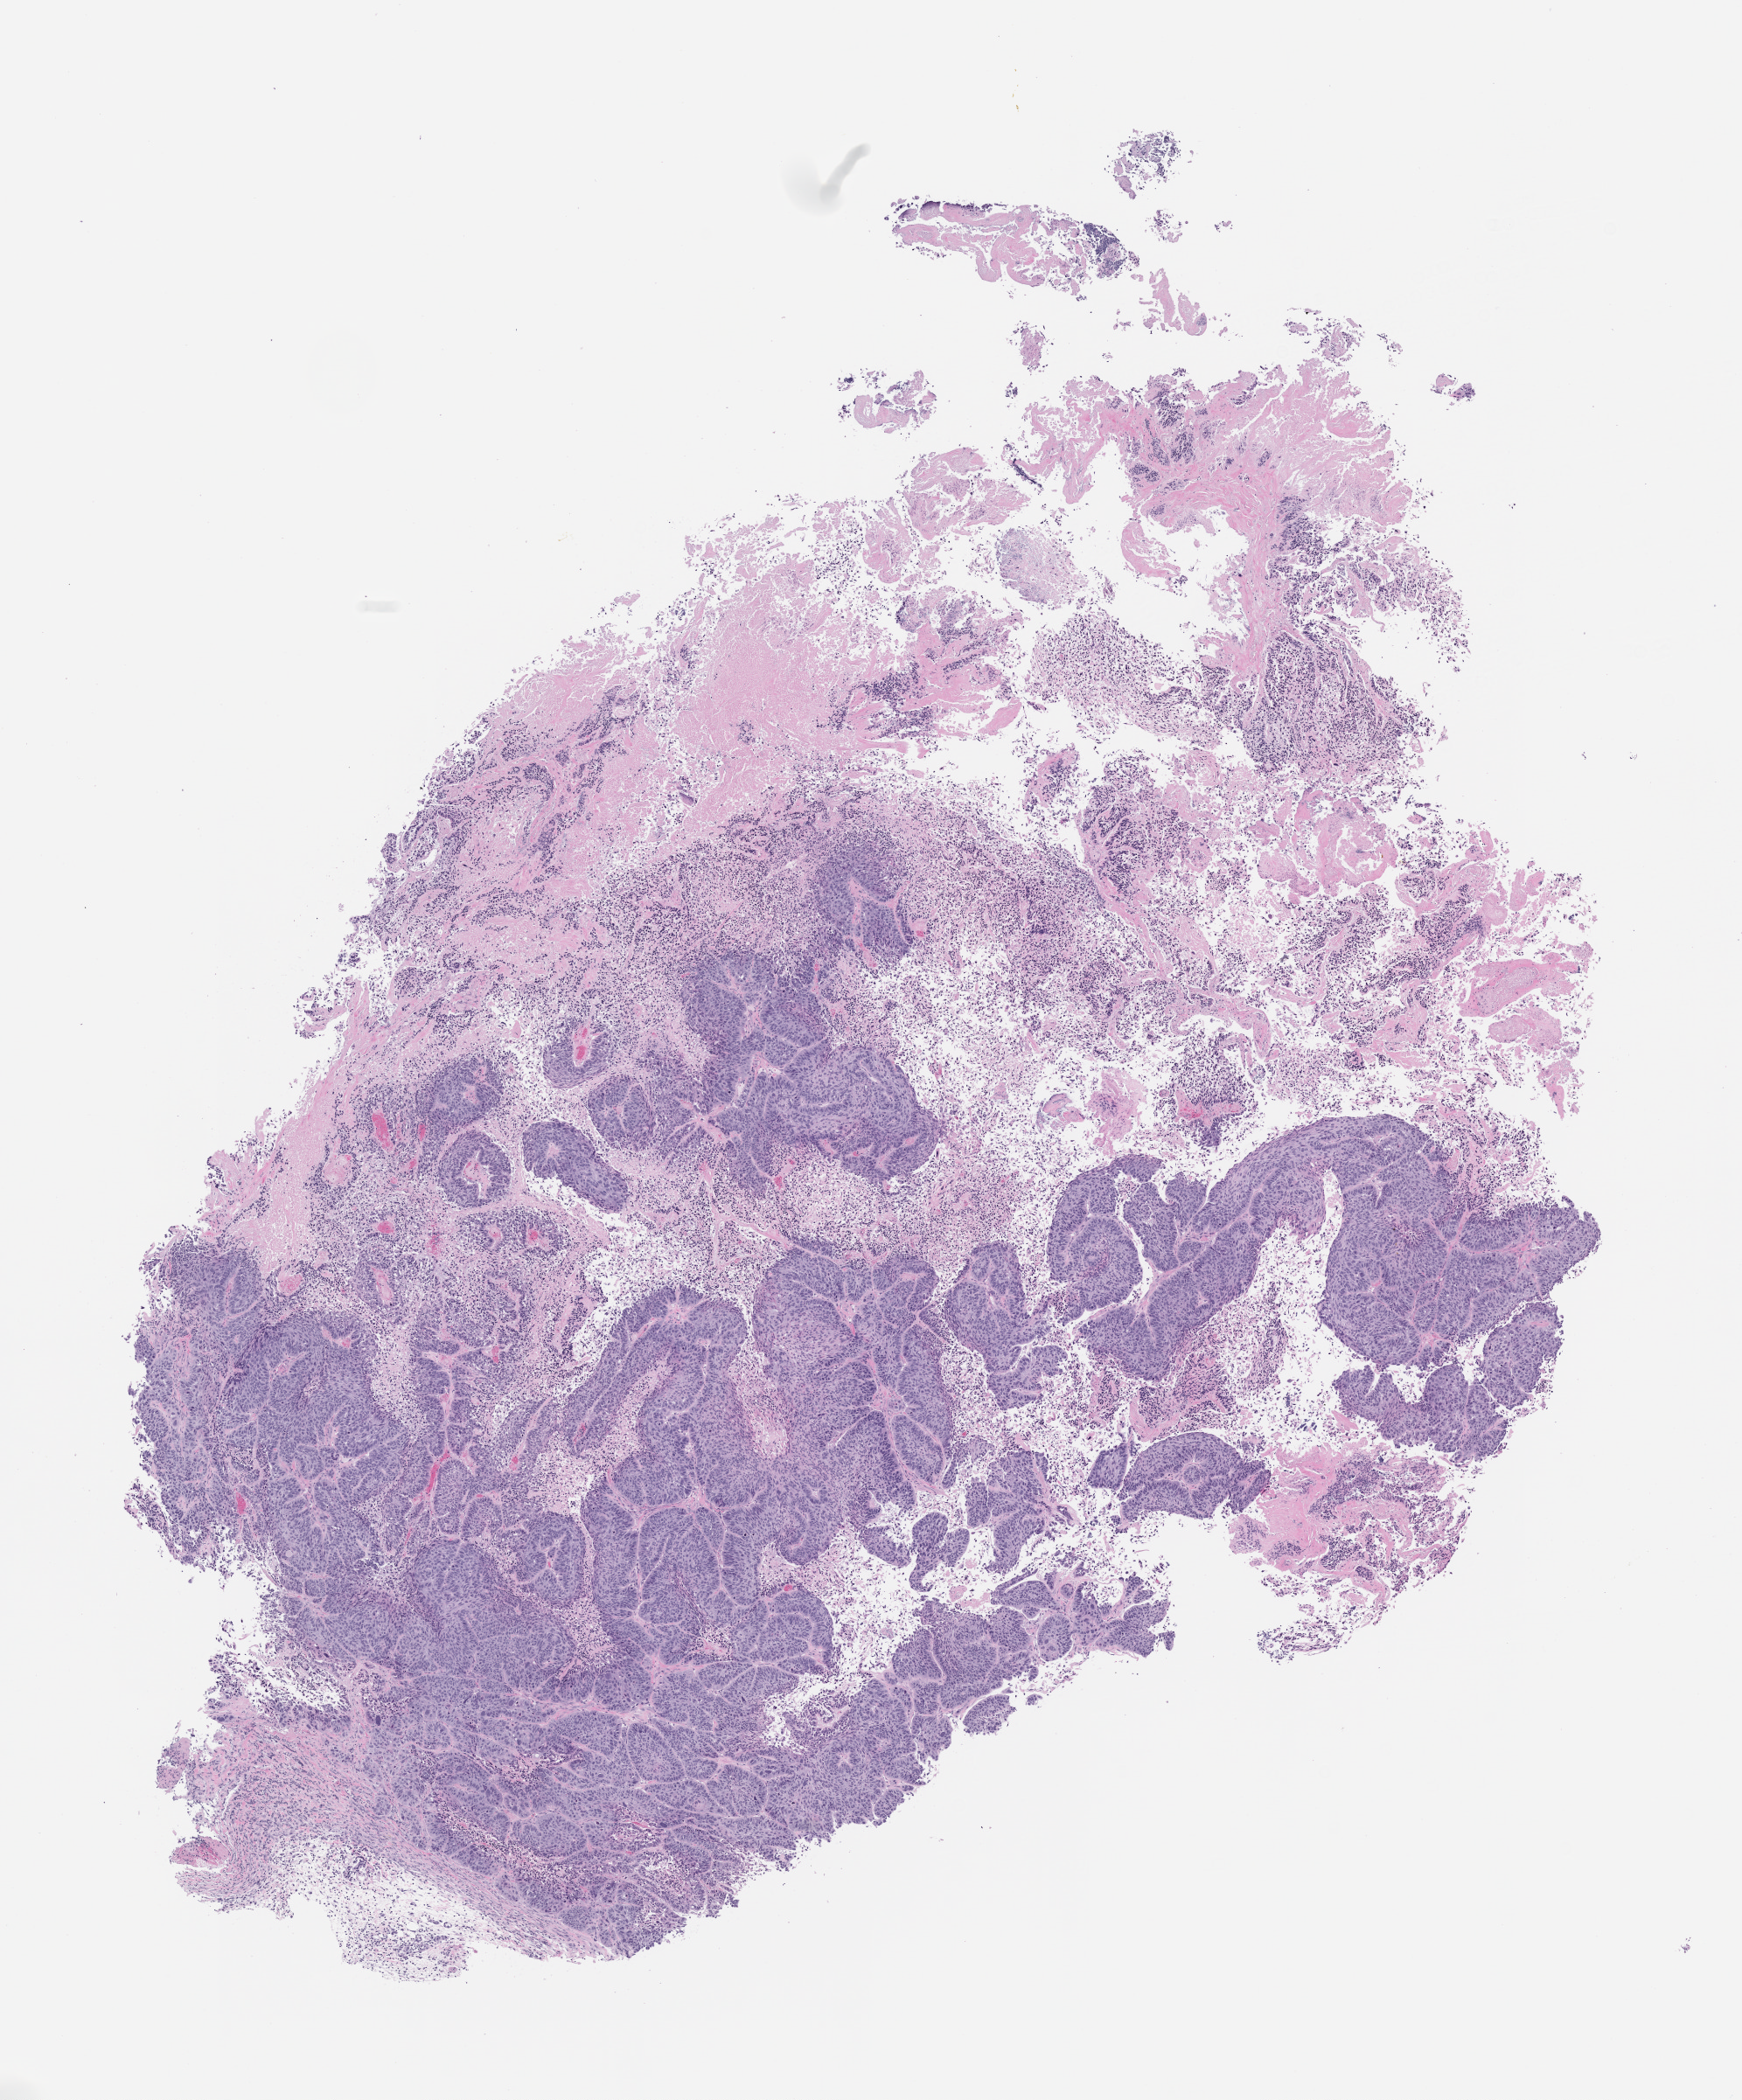
Haematoxylin and eosin whole-slide image of a patient-derived xenograft (PDX) tumor grown in a mouse, a low-resolution overview of the entire scanned area, about 8.0 x 9.7 mm, formalin-fixed paraffin-embedded section, originating tumor site category: lung.
* originating patient diagnosis: Lung Squamous Cell Carcinoma